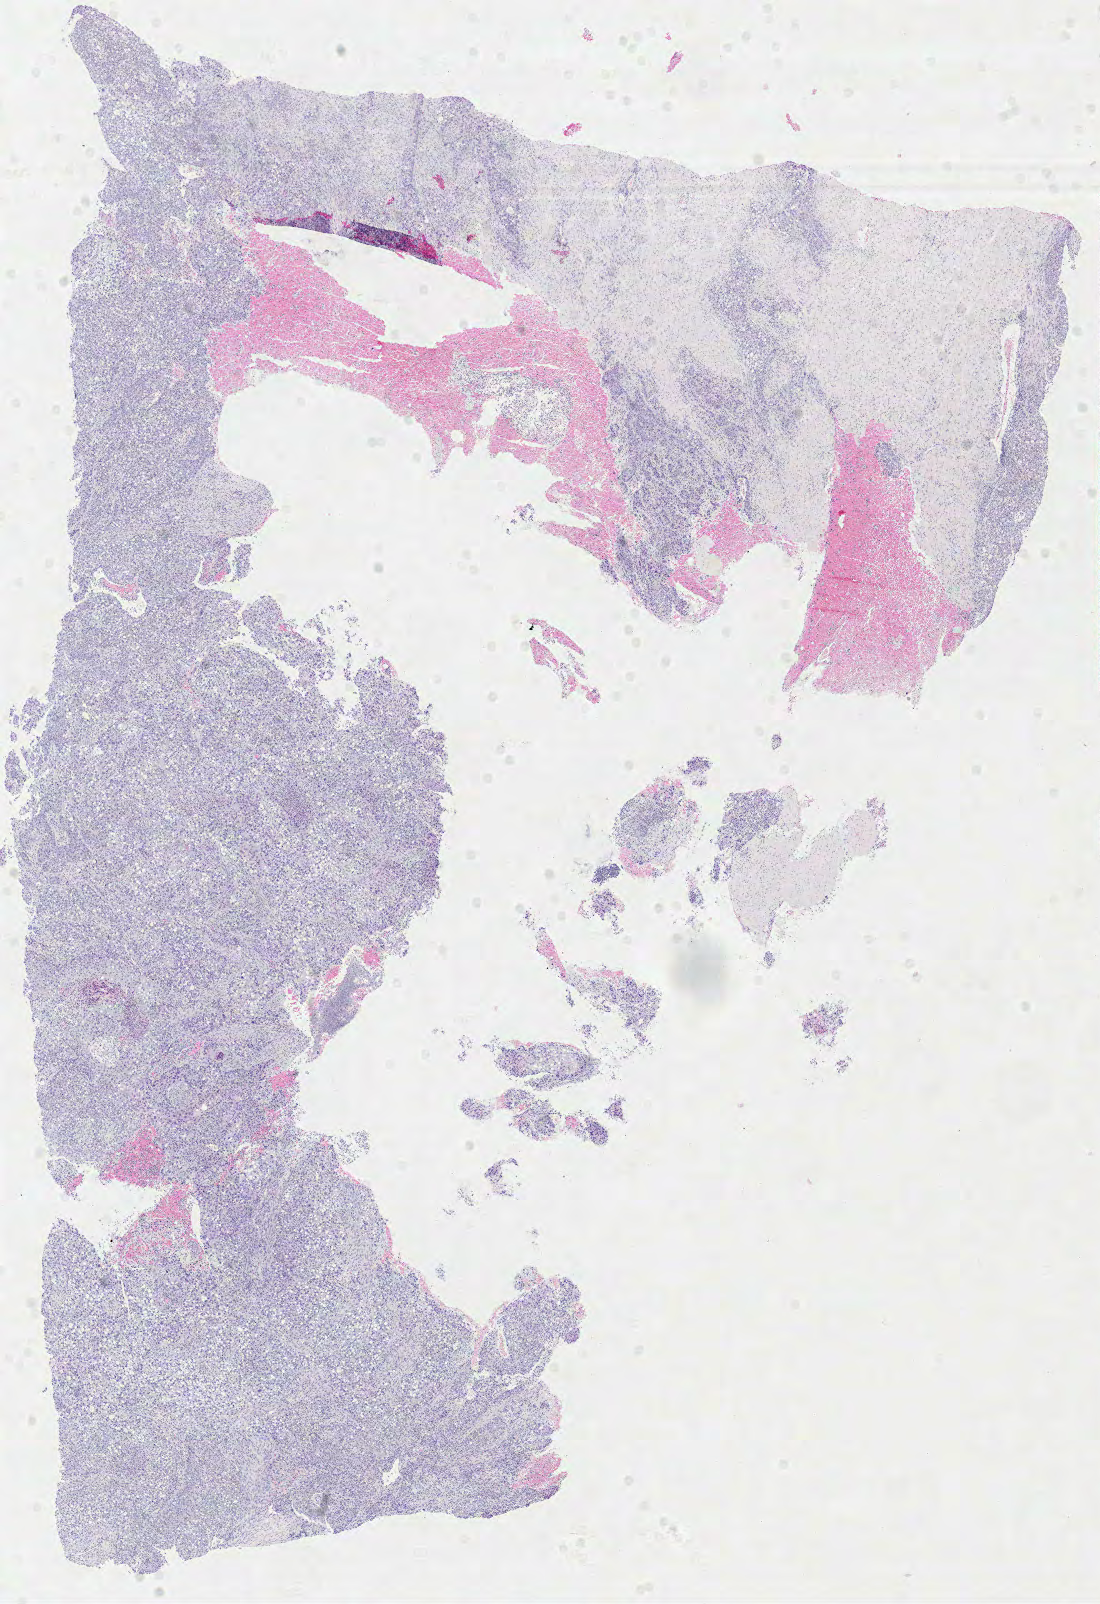
Digitized Hematoxylin and eosin (H&E) stained tissue section (whole slide), a low-resolution overview of the entire scanned area, about 8.7 x 12.6 mm (slide scanned at 40x). FFPE section. Sample: primary tumour, lung. Patient: male, age at initial diagnosis 57 years.
* histologic diagnosis: Squamous cell carcinoma, NOS (lower lobe, lung)
* laterality: left
* AJCC pathologic stage: IIB (6th edition)